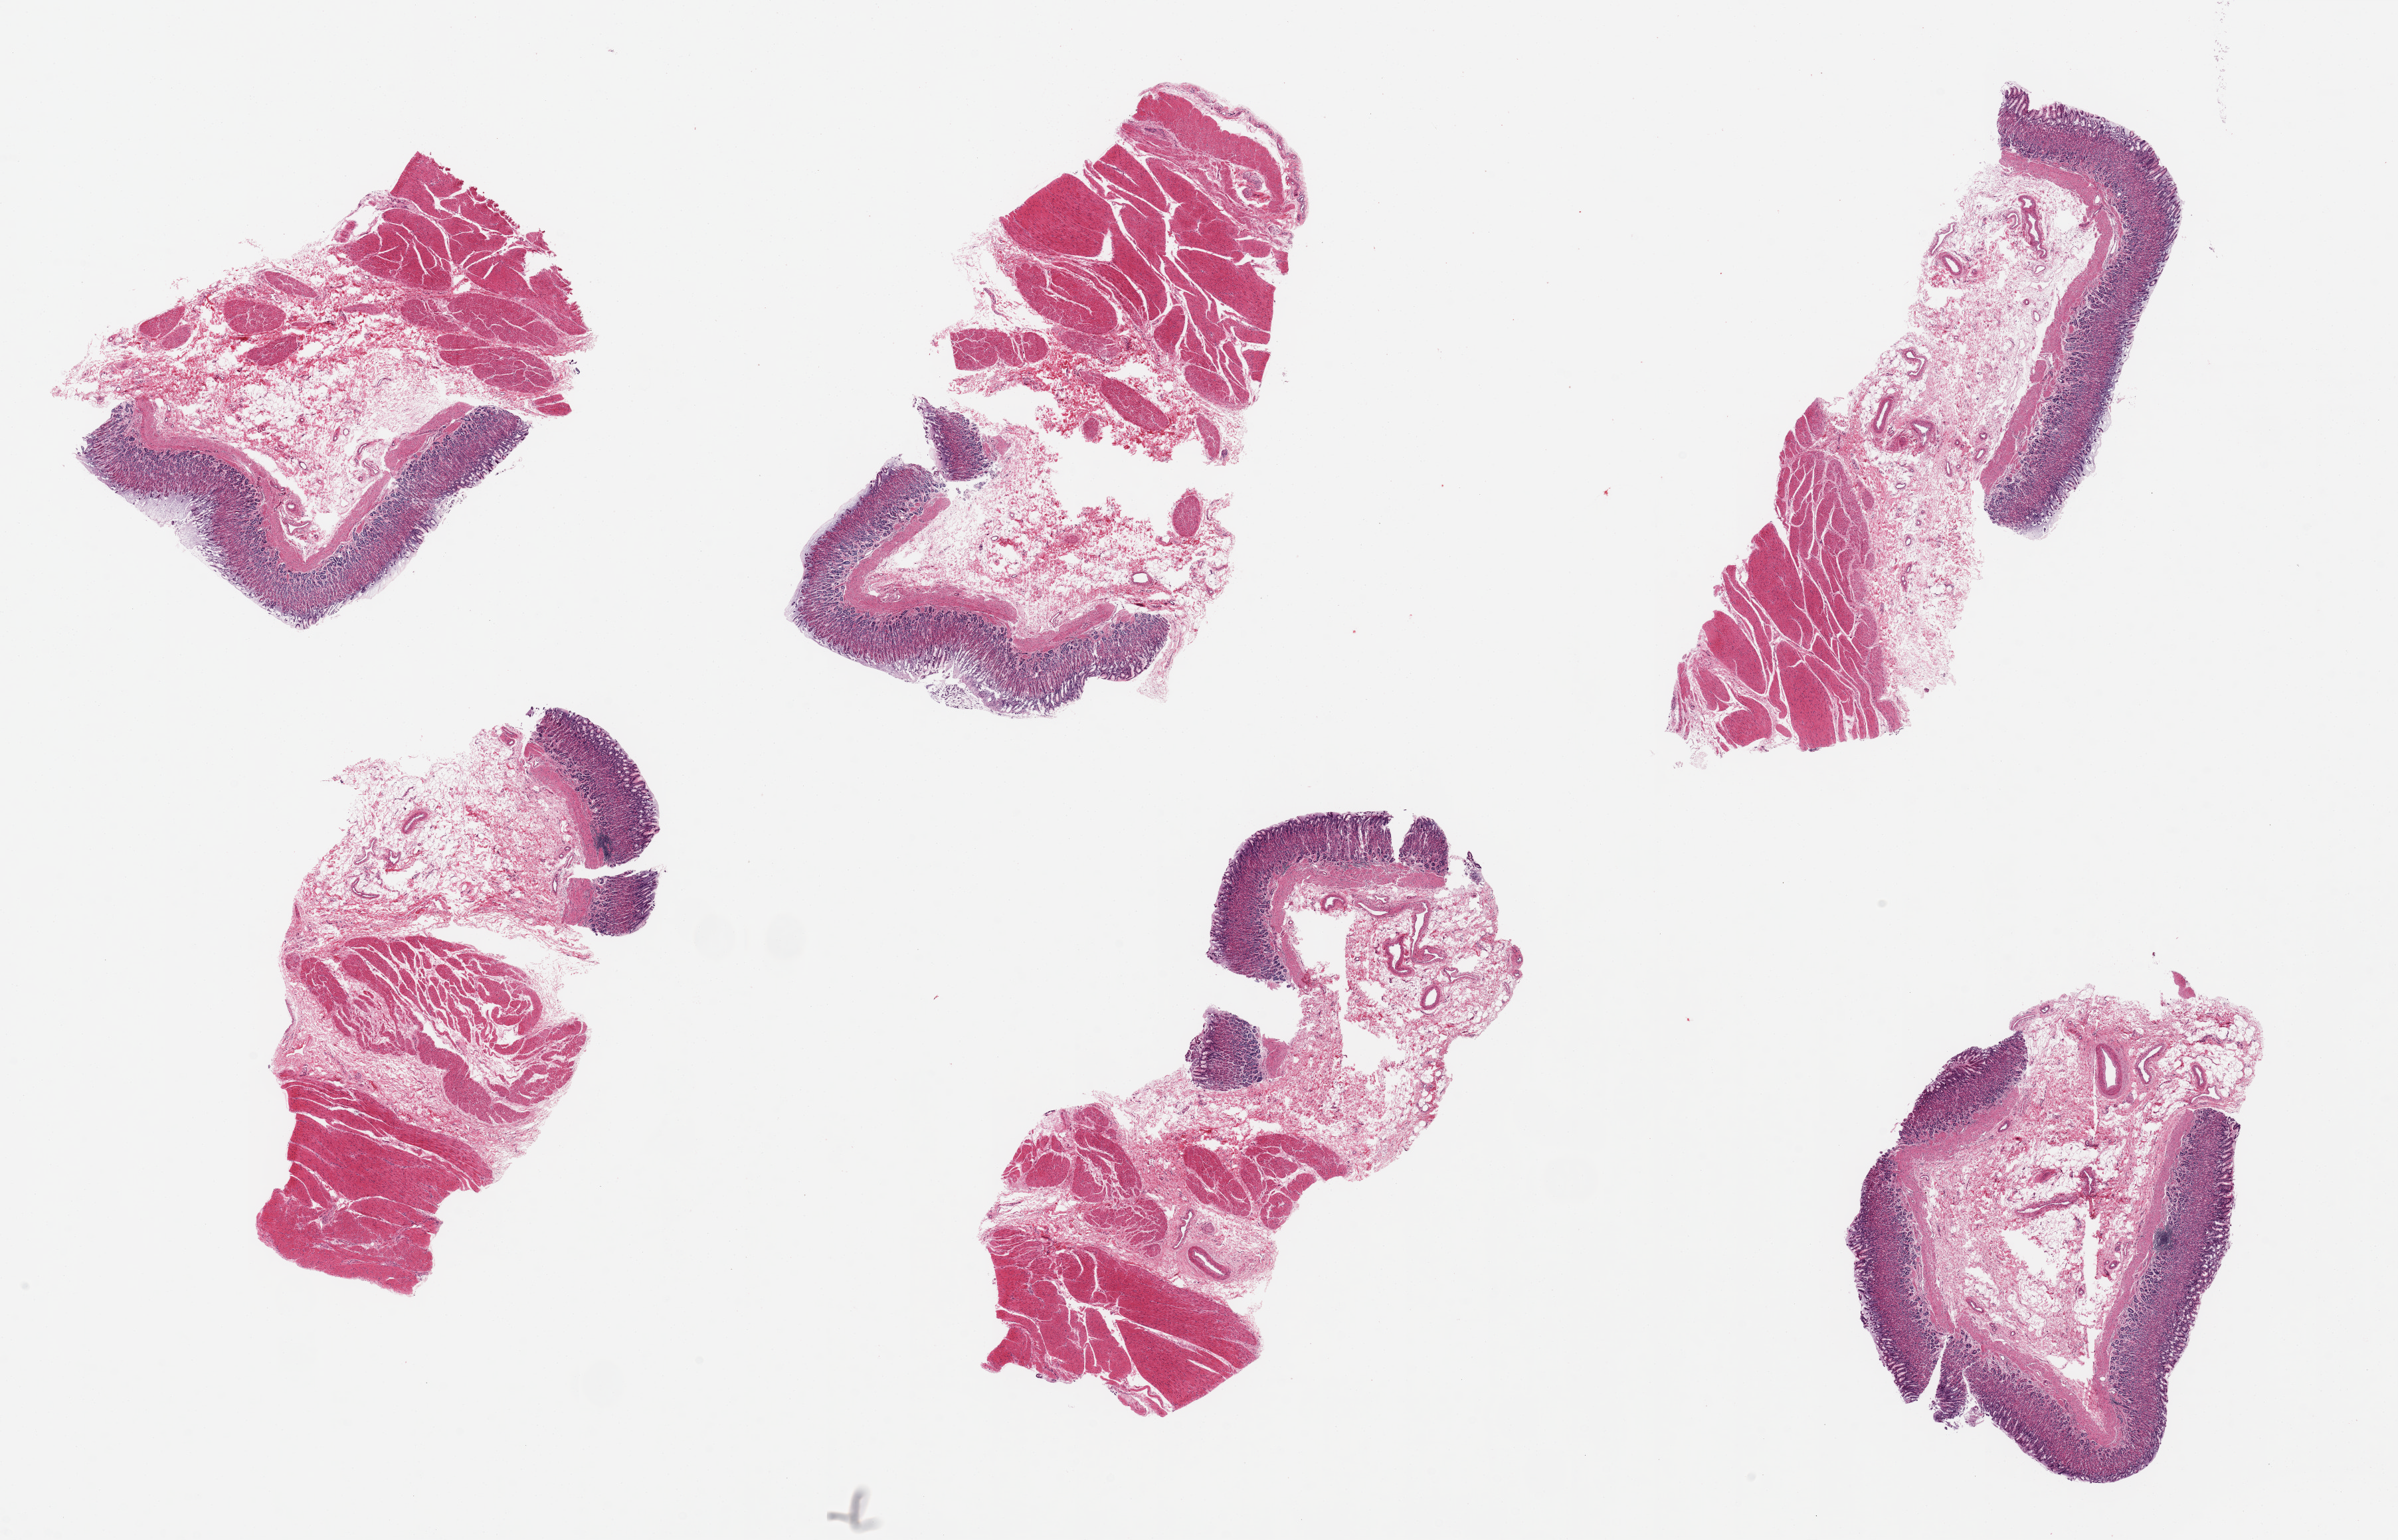
Whole-slide image, H&E stain, brightfield, low-resolution overview of the scanned area, about 28.5 x 18.3 mm, PAXgene-fixed, paraffin-embedded tissue, target tissue: stomach, tissue donor sample. Donor sex: male.
Review note (as recorded): 6 pieces, ~7.5x3mm. Mucosa up to 700microns thick, ~20-25% of thickness. Superficial 10% mucosa badly autolyzed; deeper is excellent.